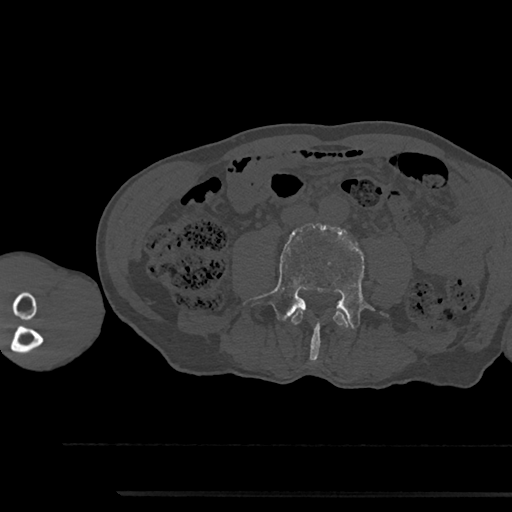
CT including the spine, one axial slice; bone window (W 1800 / L 400 HU); 0.5 mm slice thickness; 512 × 512 image matrix, field of view 367 × 367 mm. Patient: male, 79 years. Case-level facts recorded for this patient, not image findings: primary cancer: prostate.
Structures marked on this image (semi-automatically segmented with operator editing):
- L3 vertebra: bounding box <292,311,349,327> (left, top, right, bottom; pixels)
- L4 vertebra: <243,223,376,361>